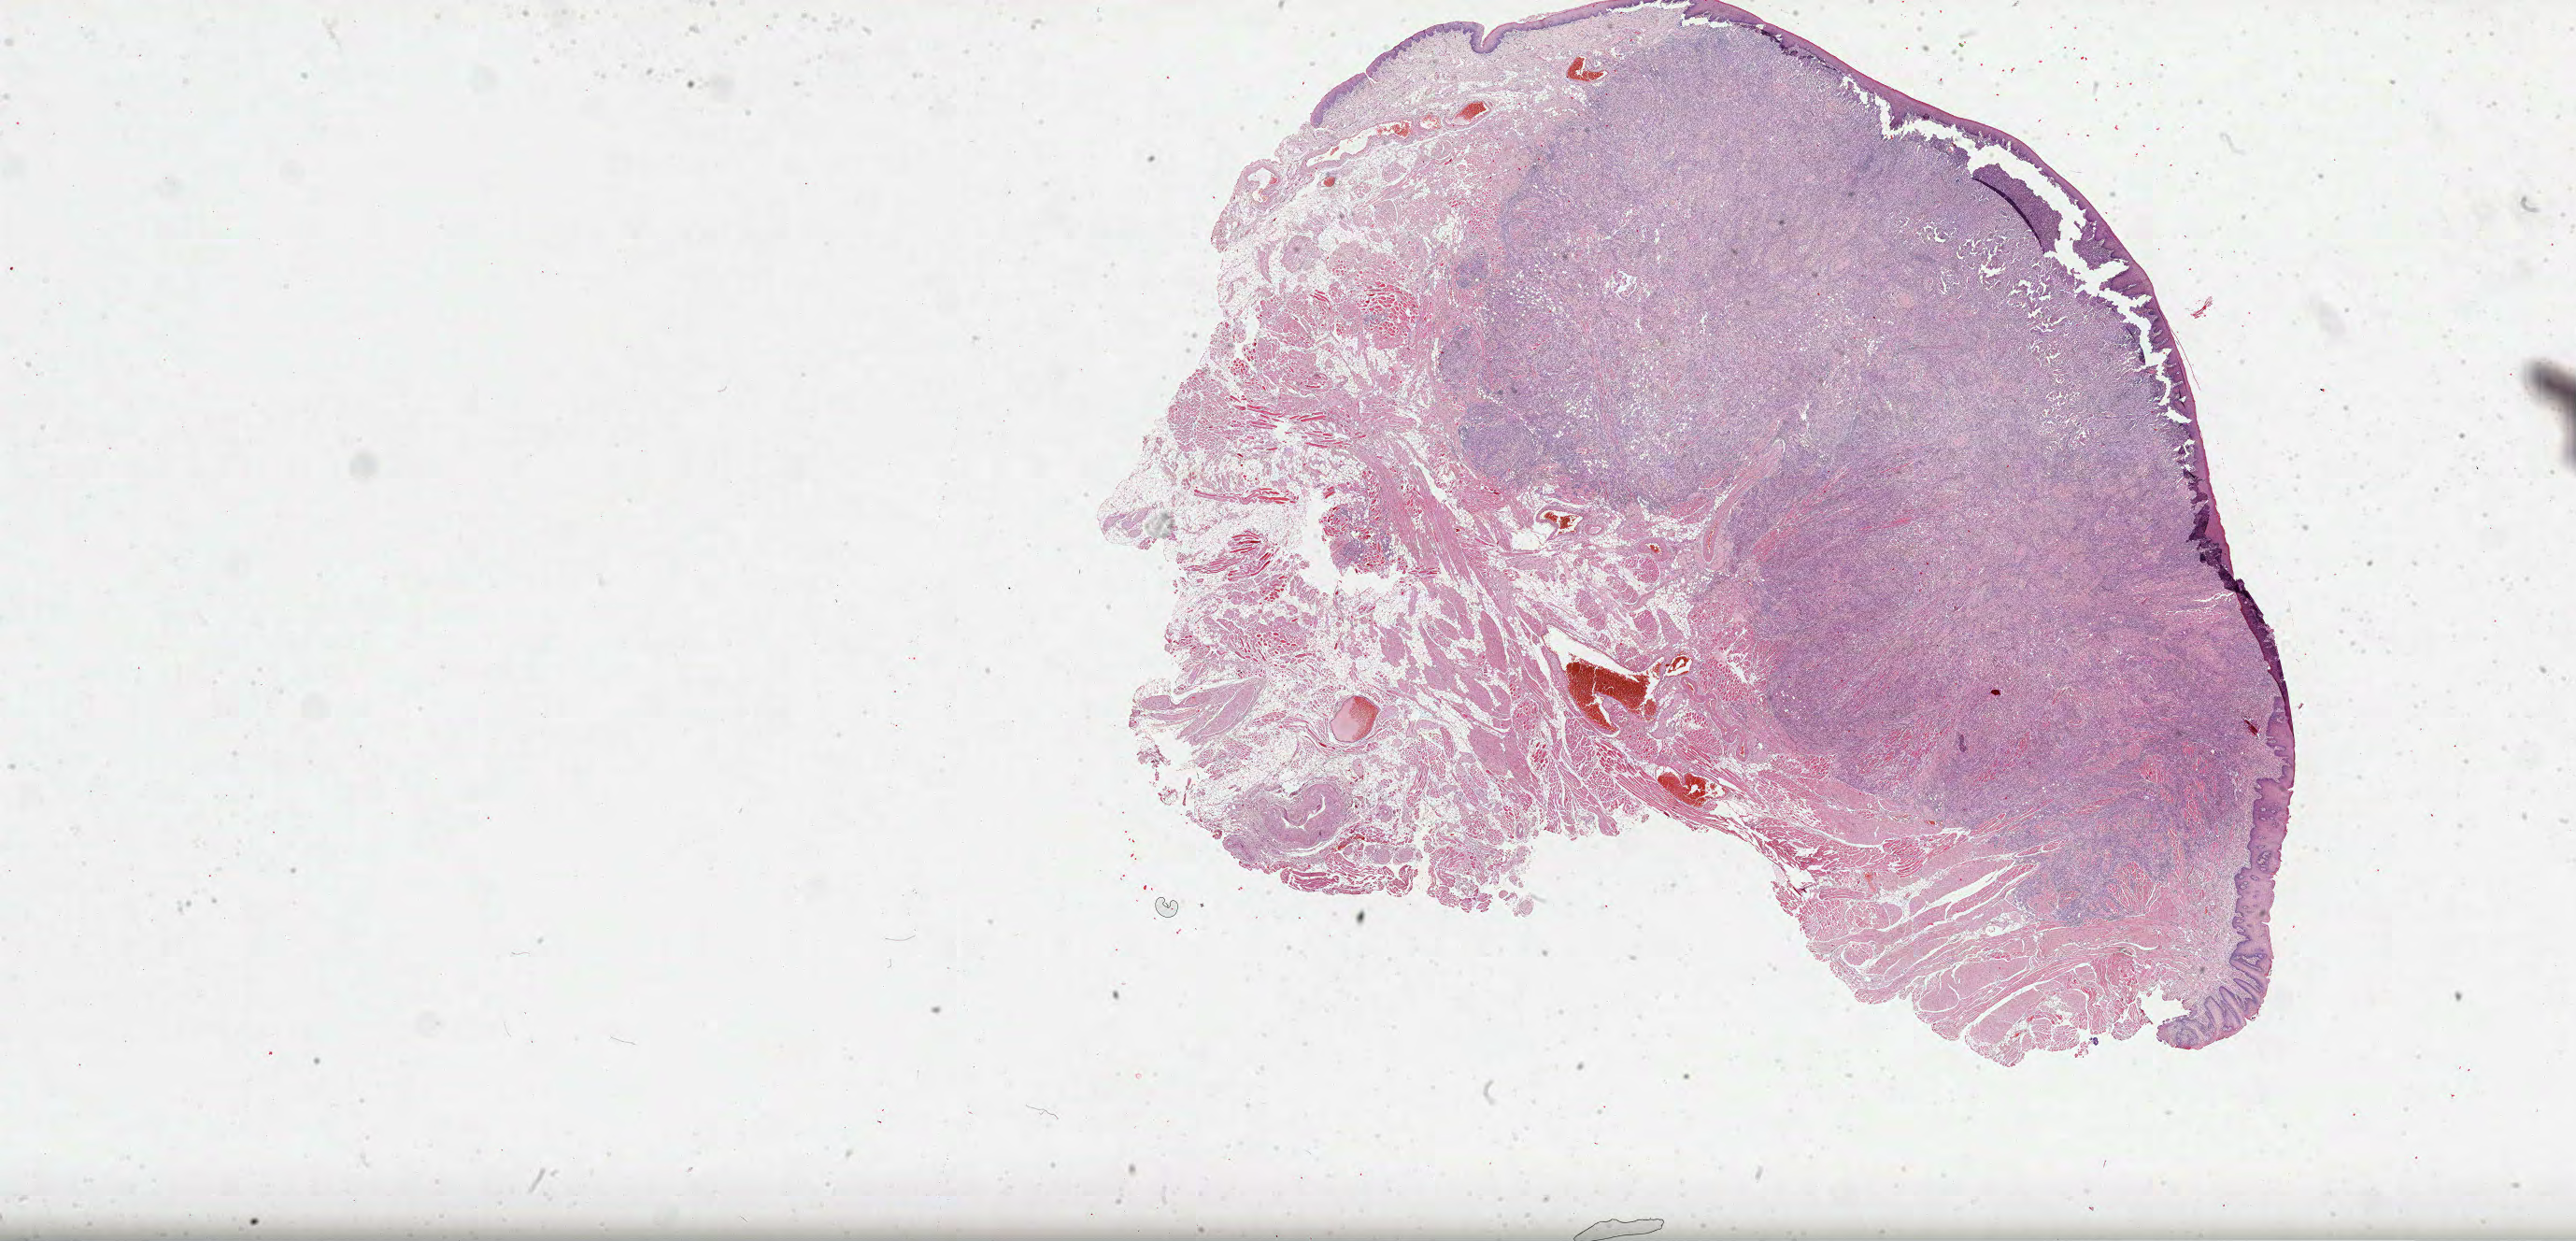
H&E whole-slide image — shown as a low-resolution overview of the whole scanned area (about 44.5 x 21.4 mm). Formalin-fixed paraffin-embedded (FFPE) diagnostic section. Primary tumour sample from the head and neck. Patient: female, age at initial diagnosis 82 years. Histologic grade: G3 (poorly differentiated).
- AJCC pathologic stage: II (7th edition)
- laterality: midline
- pathologic diagnosis: Squamous cell carcinoma, NOS
- TNM: T2 N0